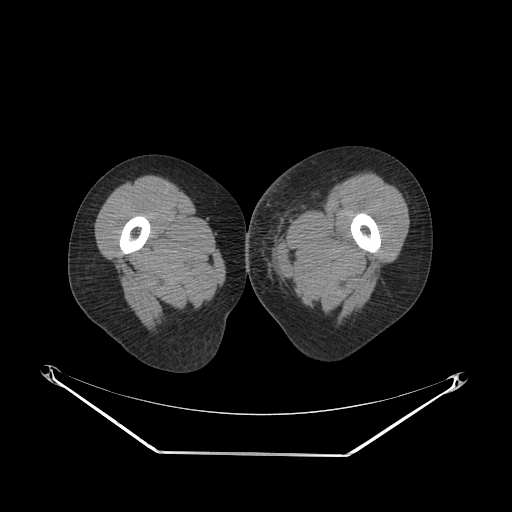
CT of an extremity soft-tissue mass (from a PET/CT study), one axial slice; position 40 of 267 along the scan axis; reconstruction kernel SOFT; soft-tissue window (W 400 / L 40 HU); 512 × 512 image matrix. Female patient. From the clinical record (not read from this slice): histological type: leiomyosarcoma; grade: high; site of the primary tumour: groin.
Structures marked on this image (expert contour drawn on MRI and transferred to this co-registered scan by the dataset authors):
- gross tumour volume including surrounding oedema: bounding box (x1, y1, x2, y2) in pixels: (246, 192, 328, 259)